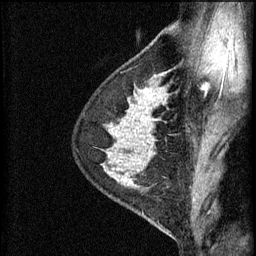
Breast MRI (dynamic contrast-enhanced), one sagittal slice; slice 43 of 60 in the series (ordered by position); 3 images stored at this slice position (order not interpretable as contrast timing); 1.5 T; TE 4.2 ms, TR 11 ms; 256 × 256 image matrix, field of view 180 × 180 mm. Female patient, age 29 years.
Outlined on this slice (semi-automatically segmented with operator editing):
- analysis volume of interest (the breast-tissue region the enhancement analysis was run in; not a lesion): box from (x=105, y=172) to (x=165, y=227) px
- tumour enhancement mask (voxels above the 70 % enhancement threshold inside the analysis volume of interest): (x=129, y=178)–(x=140, y=189)